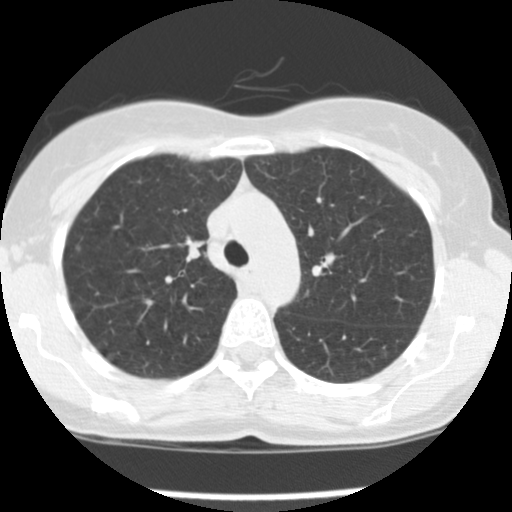
Low-dose screening chest CT, one axial slice; slice 112 of 157 in the series (ordered by position); reconstruction kernel STANDARD; 120 kVp; lung window (W 1500 / L -600 HU); 2.5 mm slice thickness; 512 × 512 image matrix, field of view 282 × 282 mm.
Structures marked on this image (outlined manually by an expert reader):
- lesion 1 (tumor, upper lobe of right lung): box from (x=184, y=236) to (x=205, y=261) px